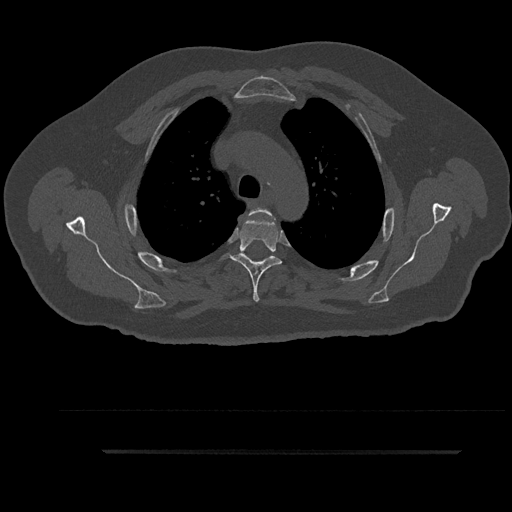
CT including the spine, one axial slice; position 674 of 797 along the scan axis; reconstruction kernel Br40s/3; 120 kVp; bone window (W 1800 / L 400 HU); 0.5 mm slice thickness; 512 × 512 image matrix. Patient: male, 63 years. From the clinical record (not read from this slice): primary cancer: renal; vertebrae with lytic lesions (as recorded): T8.
Annotated regions visible in this slice (semi-automatically segmented with operator editing):
- T3 vertebra: bounding box <247,207,272,259> (left, top, right, bottom; pixels)
- T4 vertebra: <222,215,282,302>